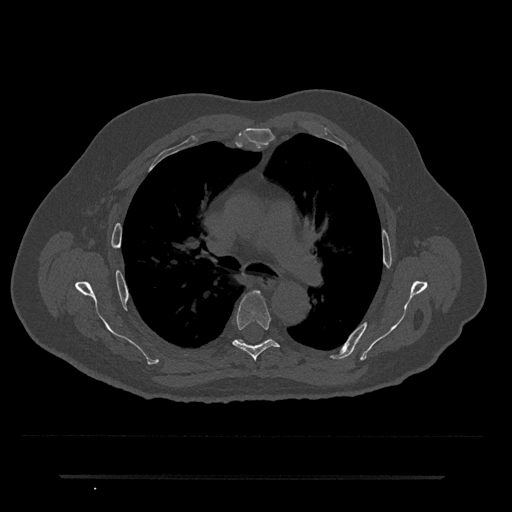
CT including the spine, one axial slice; position 480 of 797 along the scan axis; bone window (W 1800 / L 400 HU); 0.5 mm slice thickness; 512 × 512 image matrix, field of view 437 × 437 mm. Patient: male, 69 years. Case-level facts recorded for this patient, not image findings: primary cancer: prostate.
Structures marked on this image (semi-automatically segmented with operator editing):
- T5 vertebra: bounding box <232,290,280,360> (left, top, right, bottom; pixels)